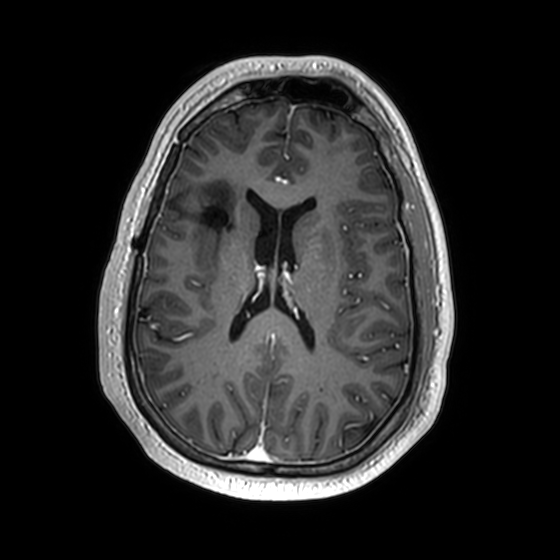
Brain MRI from a brain-tumour surgery series, one axial slice. Slice 75 of 174 in the series (ordered by position). T1-weighted post-contrast. 560 × 560 image matrix. Case-level facts recorded for this patient, not image findings: histopathology: Astrocytoma; WHO grade: 2; IDH mutation: yes; tumour location: Right Insular.
Outlined on this slice (manually delineated by an expert):
- previous resection cavity: bounding box [x1, y1, x2, y2] px = [204, 206, 229, 230]